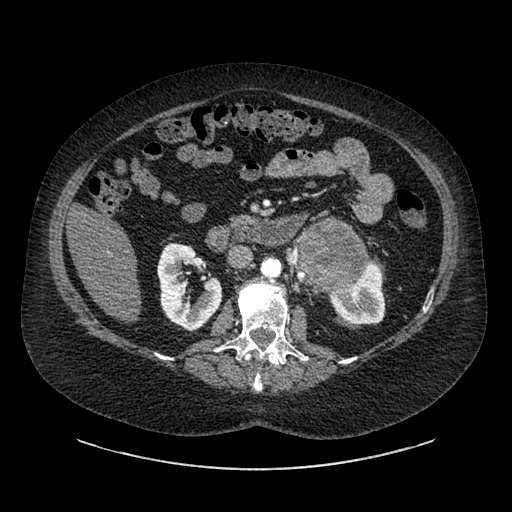
Contrast-enhanced abdominal CT, one axial slice. Slice 511 of 769 in the series (ordered by position). 120 kVp. Intravenous contrast given. Soft-tissue window (W 400 / L 40 HU). 0.62 mm slice thickness. 512 × 512 image matrix, field of view 460 × 460 mm. Patient: female, 61 years. From the clinical record (not read from this slice): diagnosis: adrenocortical carcinoma; tumour side: left adrenal.
Outlined on this slice (semi-automatic segmentation, software-assisted and operator-edited):
- mass: bounding box <299,223,366,287> (left, top, right, bottom; pixels)